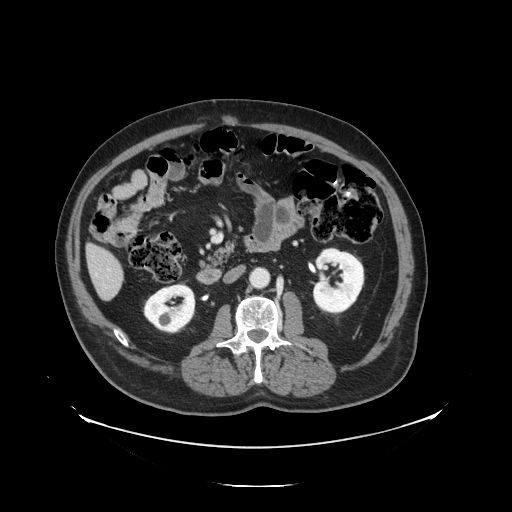
Contrast-enhanced abdominal CT, one axial slice; position 41 of 138 along the scan axis; reconstruction kernel STANDARD; 120 kVp; intravenous contrast given; soft-tissue window (W 400 / L 40 HU); 2.5 mm slice thickness; 512 × 512 image matrix, field of view 497 × 497 mm. Male patient, age 77 years. Case-level facts recorded for this patient, not image findings: diagnosis: colorectal cancer liver metastases, imaged before liver resection; multiple liver metastases: no; largest metastasis: 1.5 cm; disease in both lobes: no.
Outlined on this slice (expert manual segmentation):
- liver: bounding box <88,246,124,300> (left, top, right, bottom; pixels)
- planned liver remnant (the part of the liver to remain after resection): <88,246,120,276>